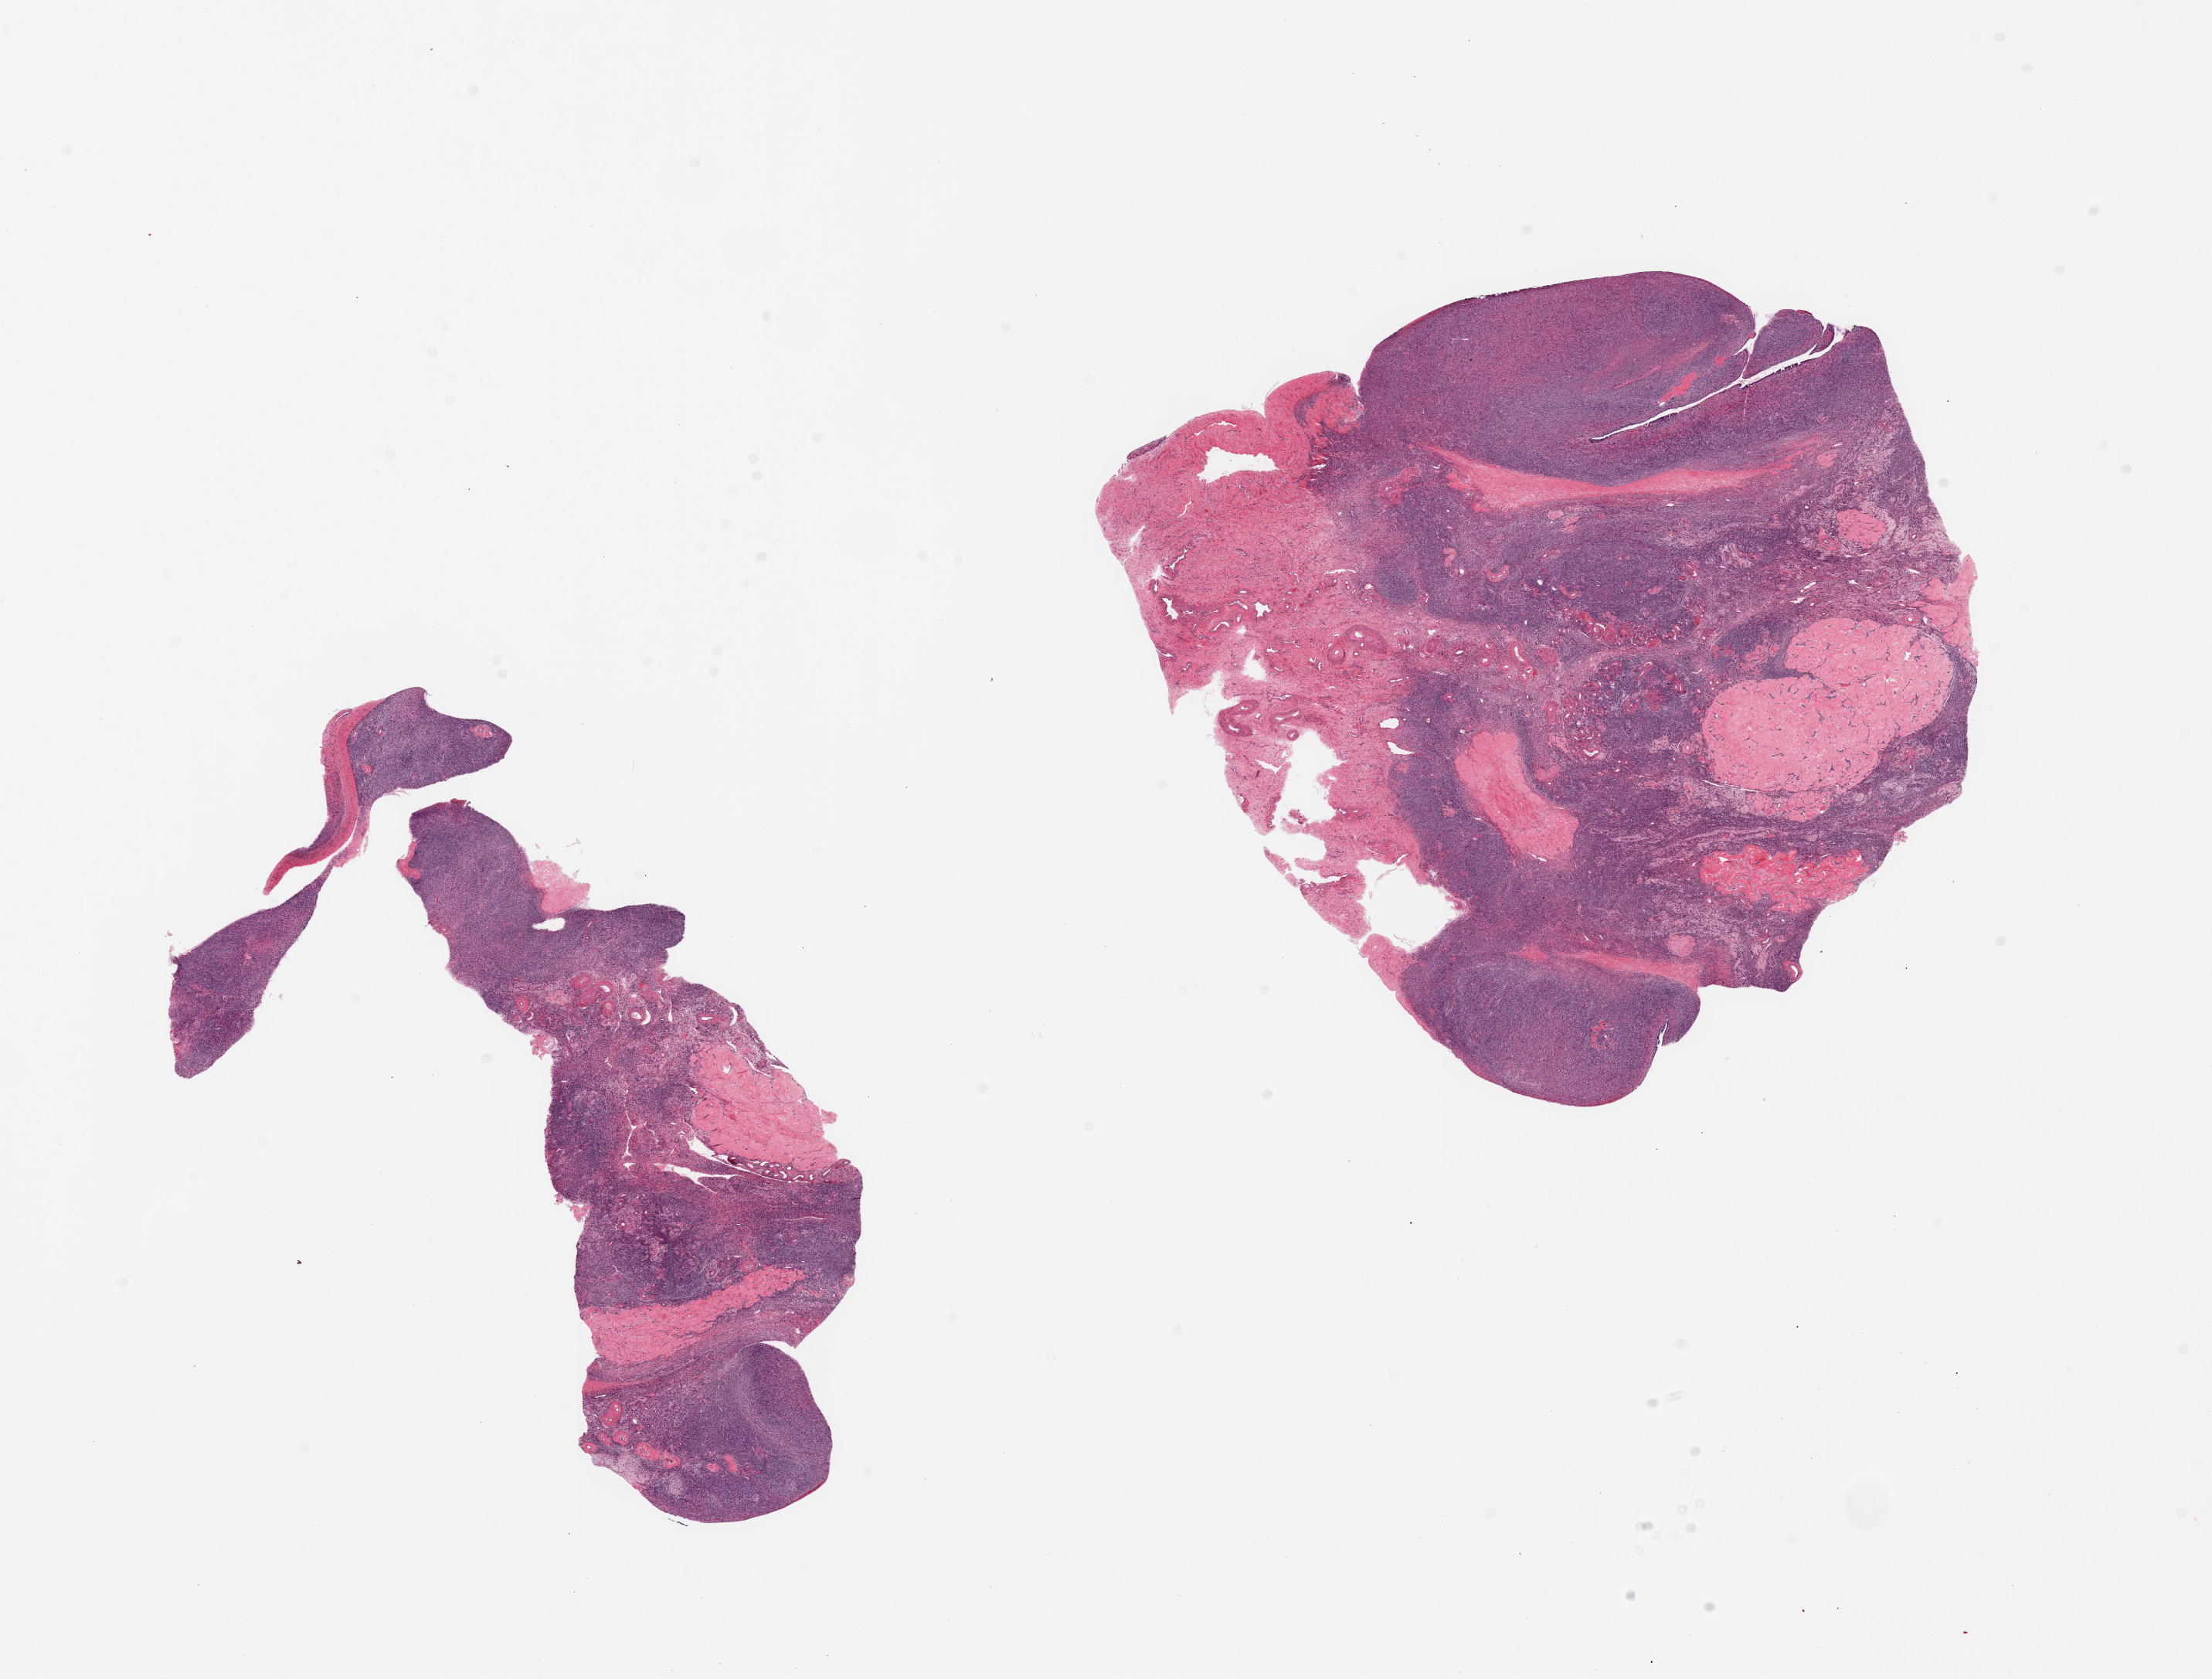
Whole-slide image, H&E stain, whole scanned area (about 22.6 x 17.2 mm) shown as a low-resolution overview. PAXgene-fixed, paraffin-embedded tissue. Section of ovary (target tissue). Tissue donor sample. Donor sex: female.
Review note (as recorded): 2 pieces, typical post menopausal atrophy.